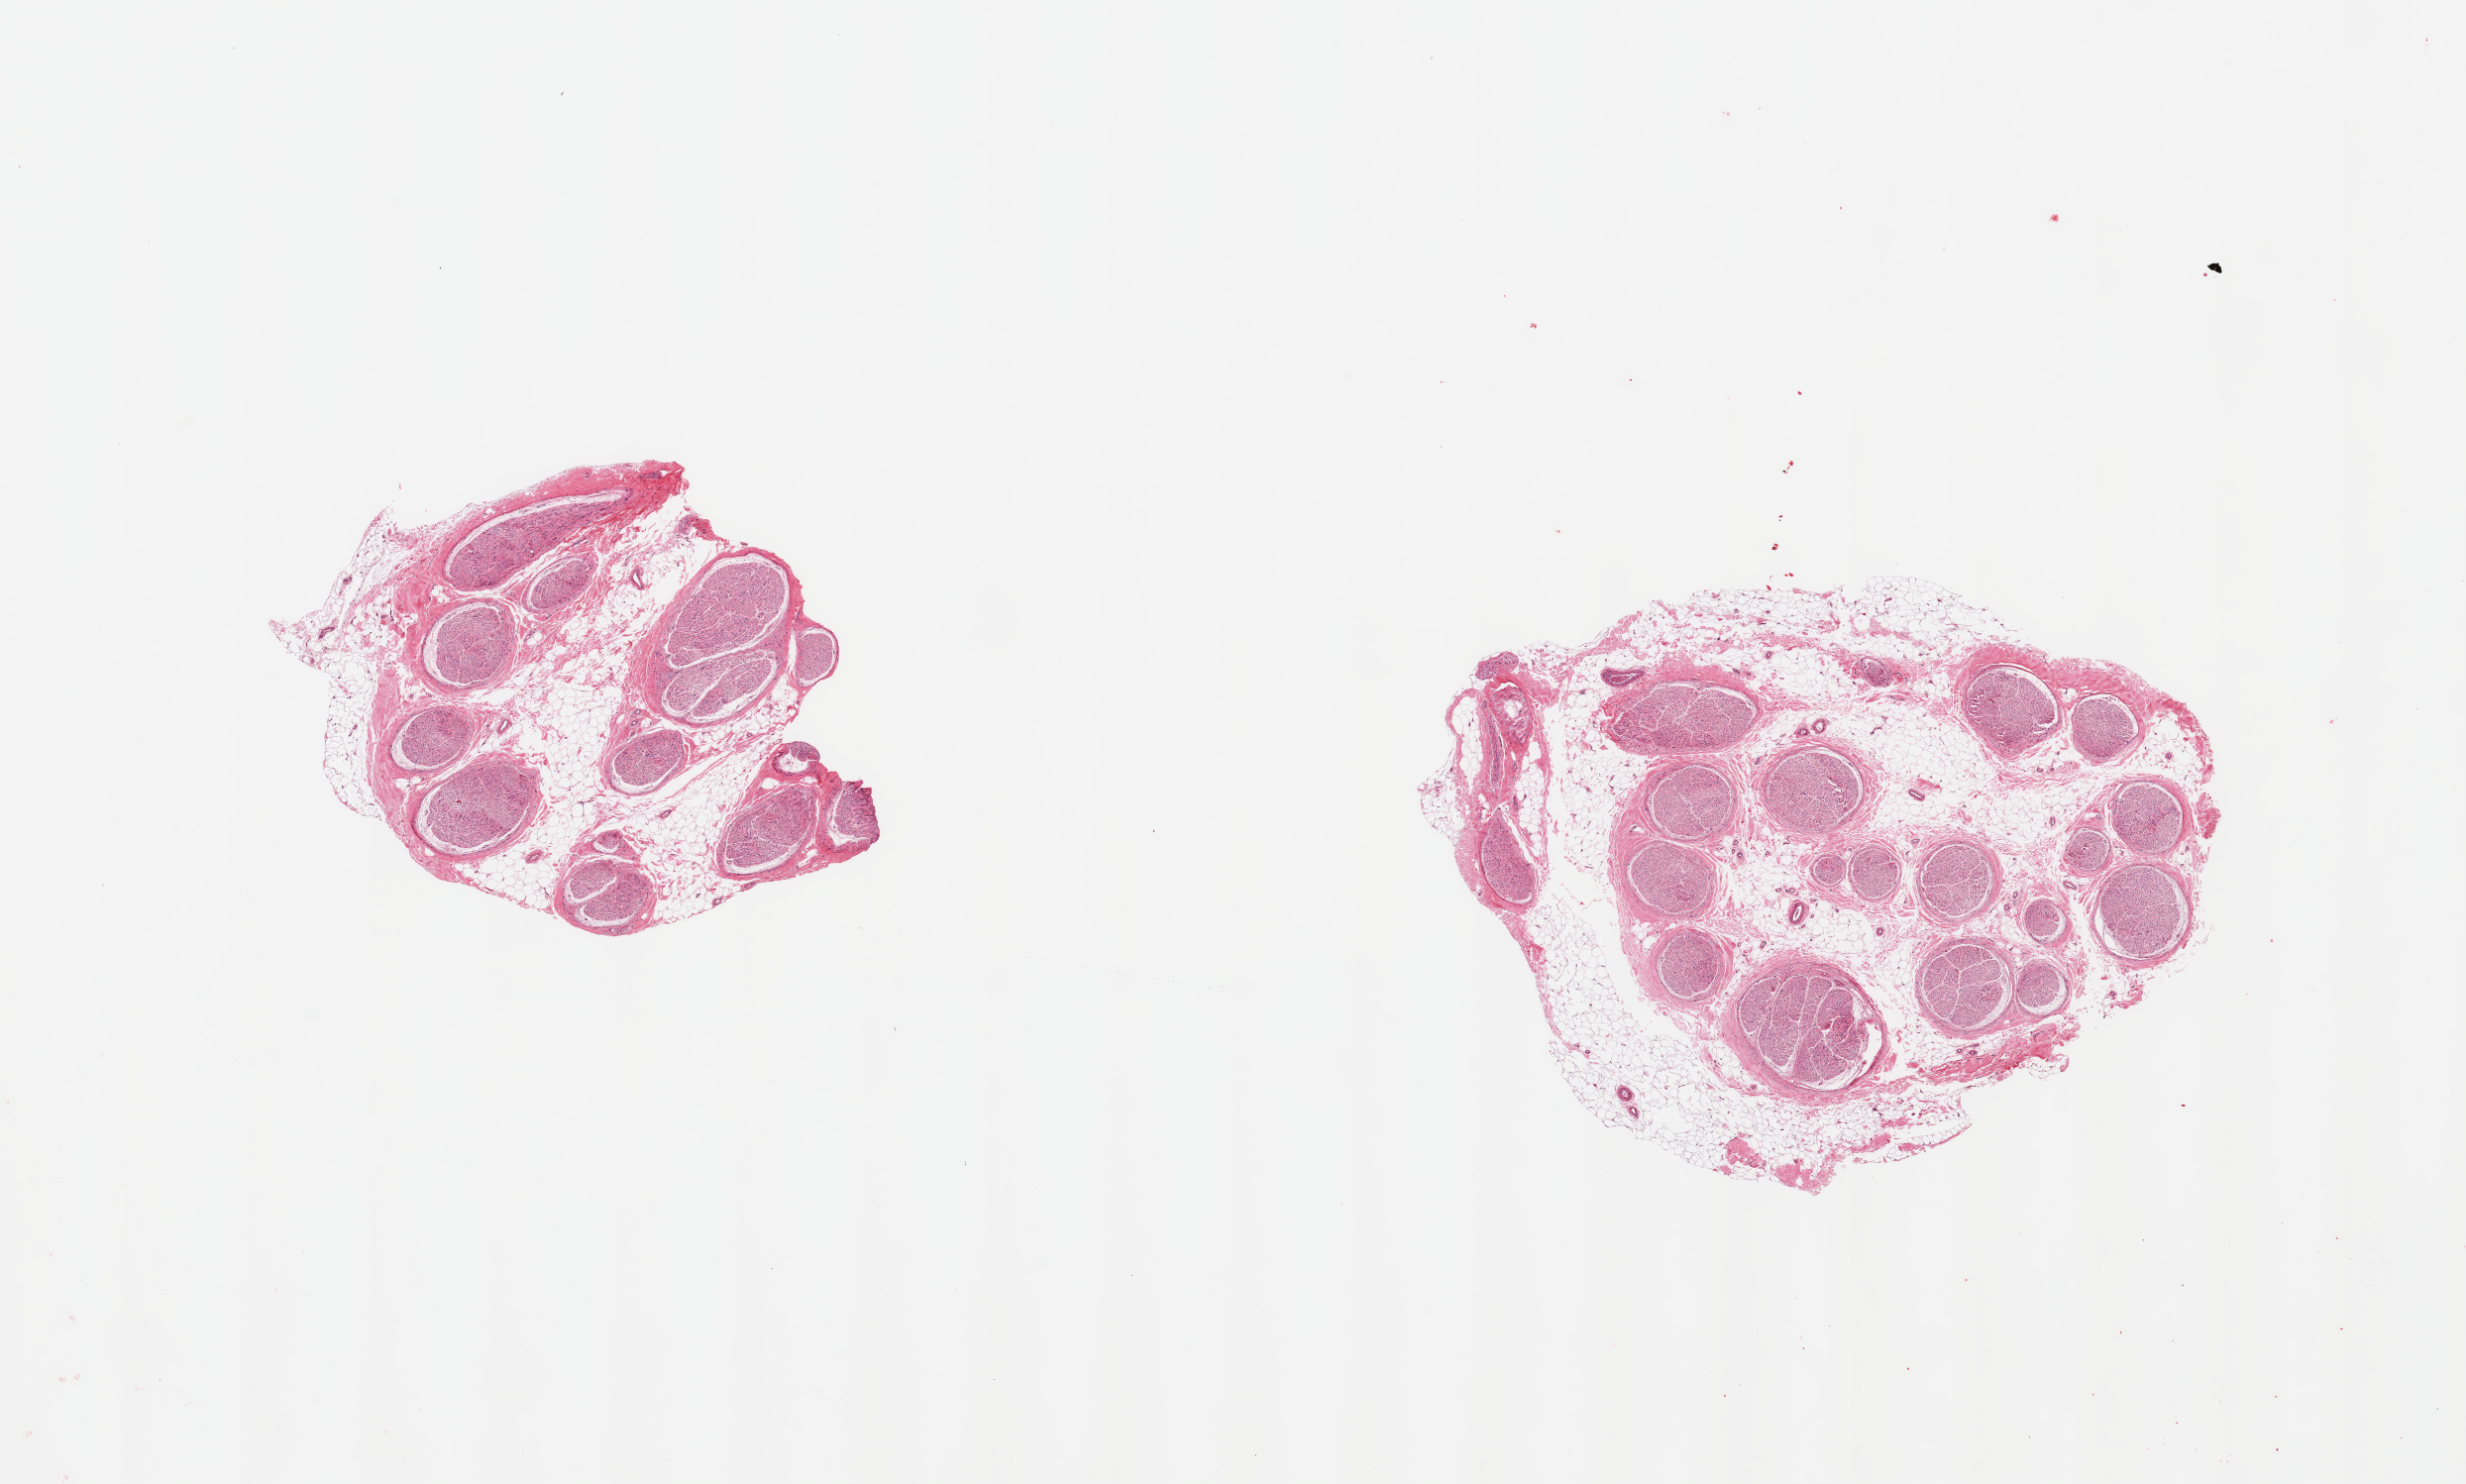
Whole-slide image, H&E stain, a low-resolution overview of the entire scanned area, about 19.7 x 11.8 mm (slide scanned at 20x). PAXgene-fixed, paraffin-embedded tissue. Target tissue: tibial nerve. Donor tissue sample. Donor: male.
Pathologist's review note for this sample: 2 pieces, rims of fat up to ~0.5mm; ~40-50% interstital fat.